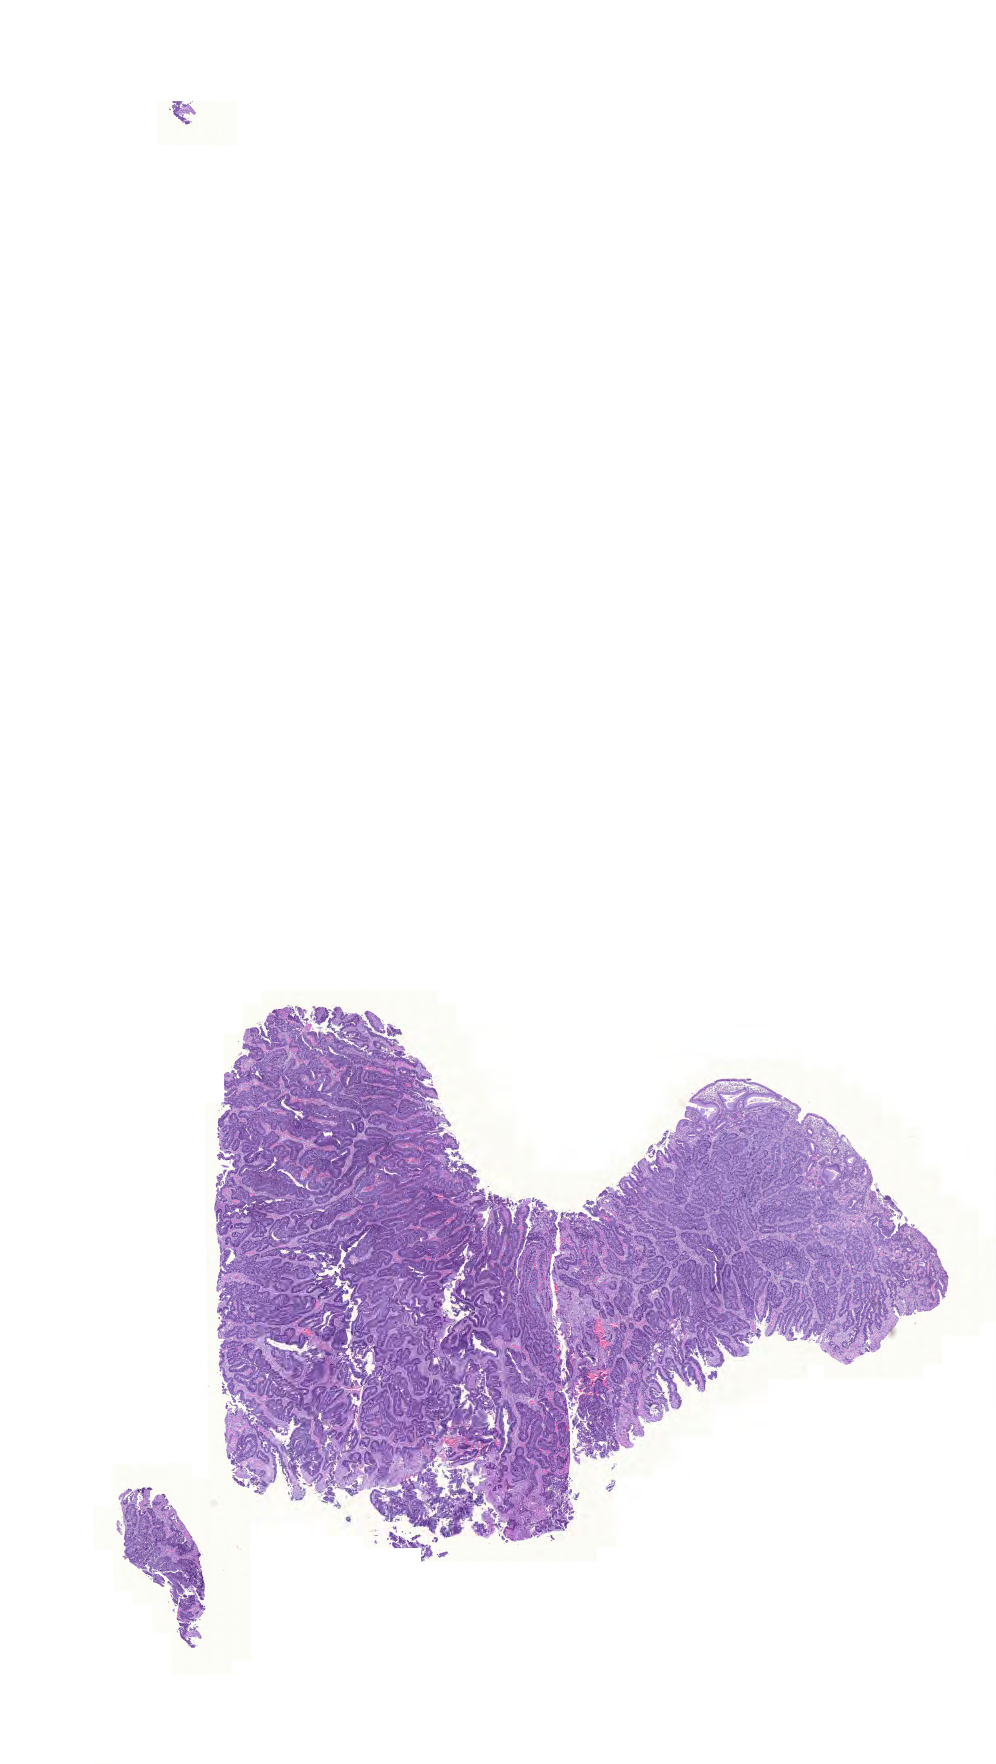
Hematoxylin and eosin (H&E) stained whole-slide image, low-resolution overview of the scanned area, about 14.8 x 26.2 mm. Formalin-fixed paraffin-embedded (FFPE) diagnostic section. Sample: primary tumour, colon. Male, age 63 years at initial diagnosis.
* AJCC pathologic stage: III (5th edition)
* diagnosis: Adenocarcinoma, NOS